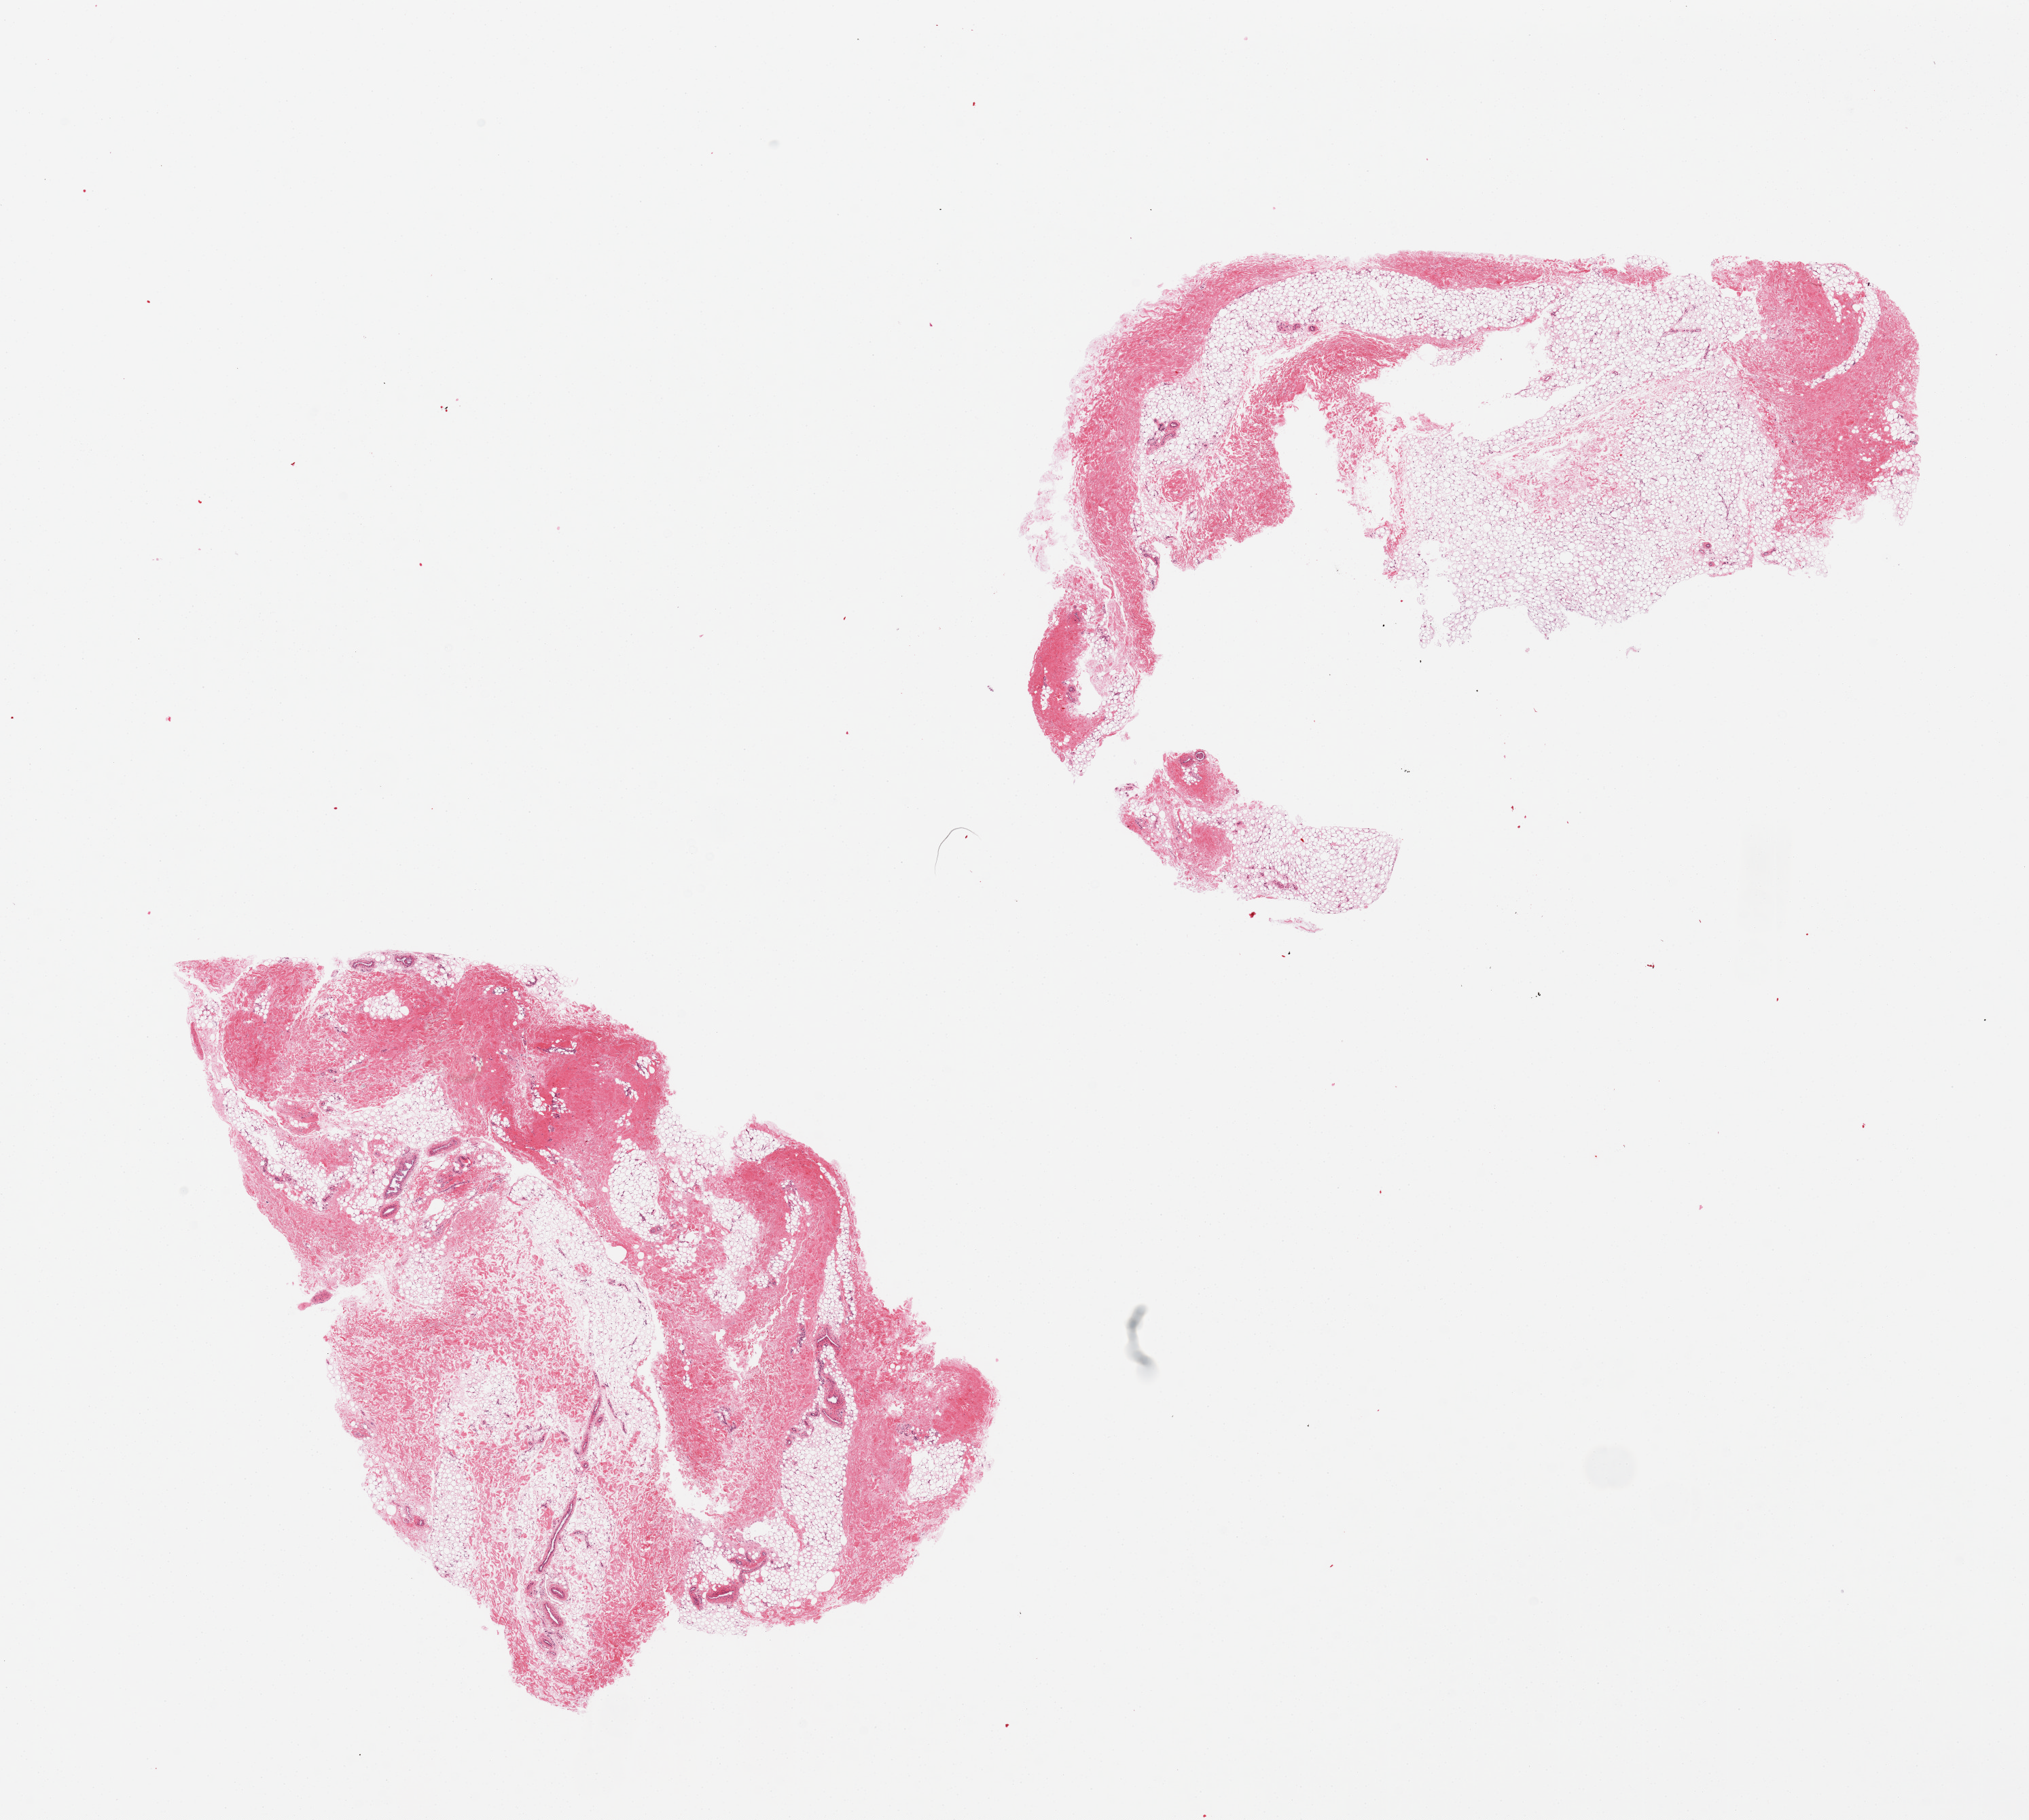
Digitized H&E-stained section, whole scanned area (about 23.6 x 21.2 mm, slide scanned at 20x) shown as a low-resolution overview. PAXgene-fixed, paraffin-embedded tissue. Section of breast (target tissue). Donor tissue sample. Male donor.
- review note (as recorded): 2 pieces; fibrofatty tissue, no ducts